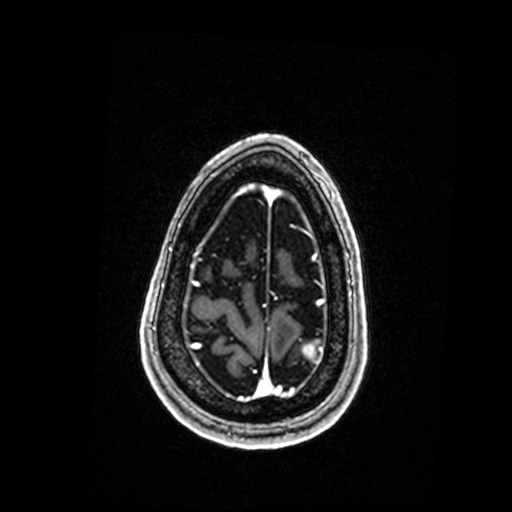
Brain MRI from a brain-tumour surgery series, one axial slice; position 36 of 192 along the scan axis; T1-weighted post-contrast; 0.98 mm slice thickness; 512 × 512 image matrix, field of view 250 × 250 mm. From the clinical record (not read from this slice): histopathology: Metastastic Carcinoma, Poorly Differentiated; tumour location: Left Parietal.
Annotated regions visible in this slice (expert manual segmentation):
- tumour: bounding box <305,346,322,362> (left, top, right, bottom; pixels)